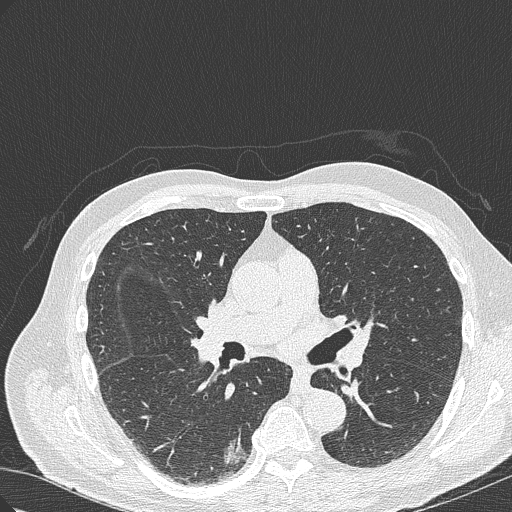
Low-dose screening chest CT, axial slice, first (baseline) screen, lung window (W 1500 / L -600 HU), 1 mm slice thickness, 512 × 512 image matrix, field of view 350 × 350 mm. Male participant, aged 70 years at enrolment.
• Expert reader's lesion annotation, bounding box <198,419,261,476> (left, top, right, bottom; pixels).
• The screening reader recorded 4 non-calcified nodules or masses ≥4 mm on this exam (right lower lobe, right lower lobe, right upper lobe, right lower lobe); which of them this box marks is not recorded.
• Participant outcome: lung cancer diagnosed 978 days after this screen — bronchiolo-alveolar adenocarcinoma, NOS, right lower lobe, poorly differentiated (G3), stage IB (AJCC 6th edition), 30 mm at pathology.